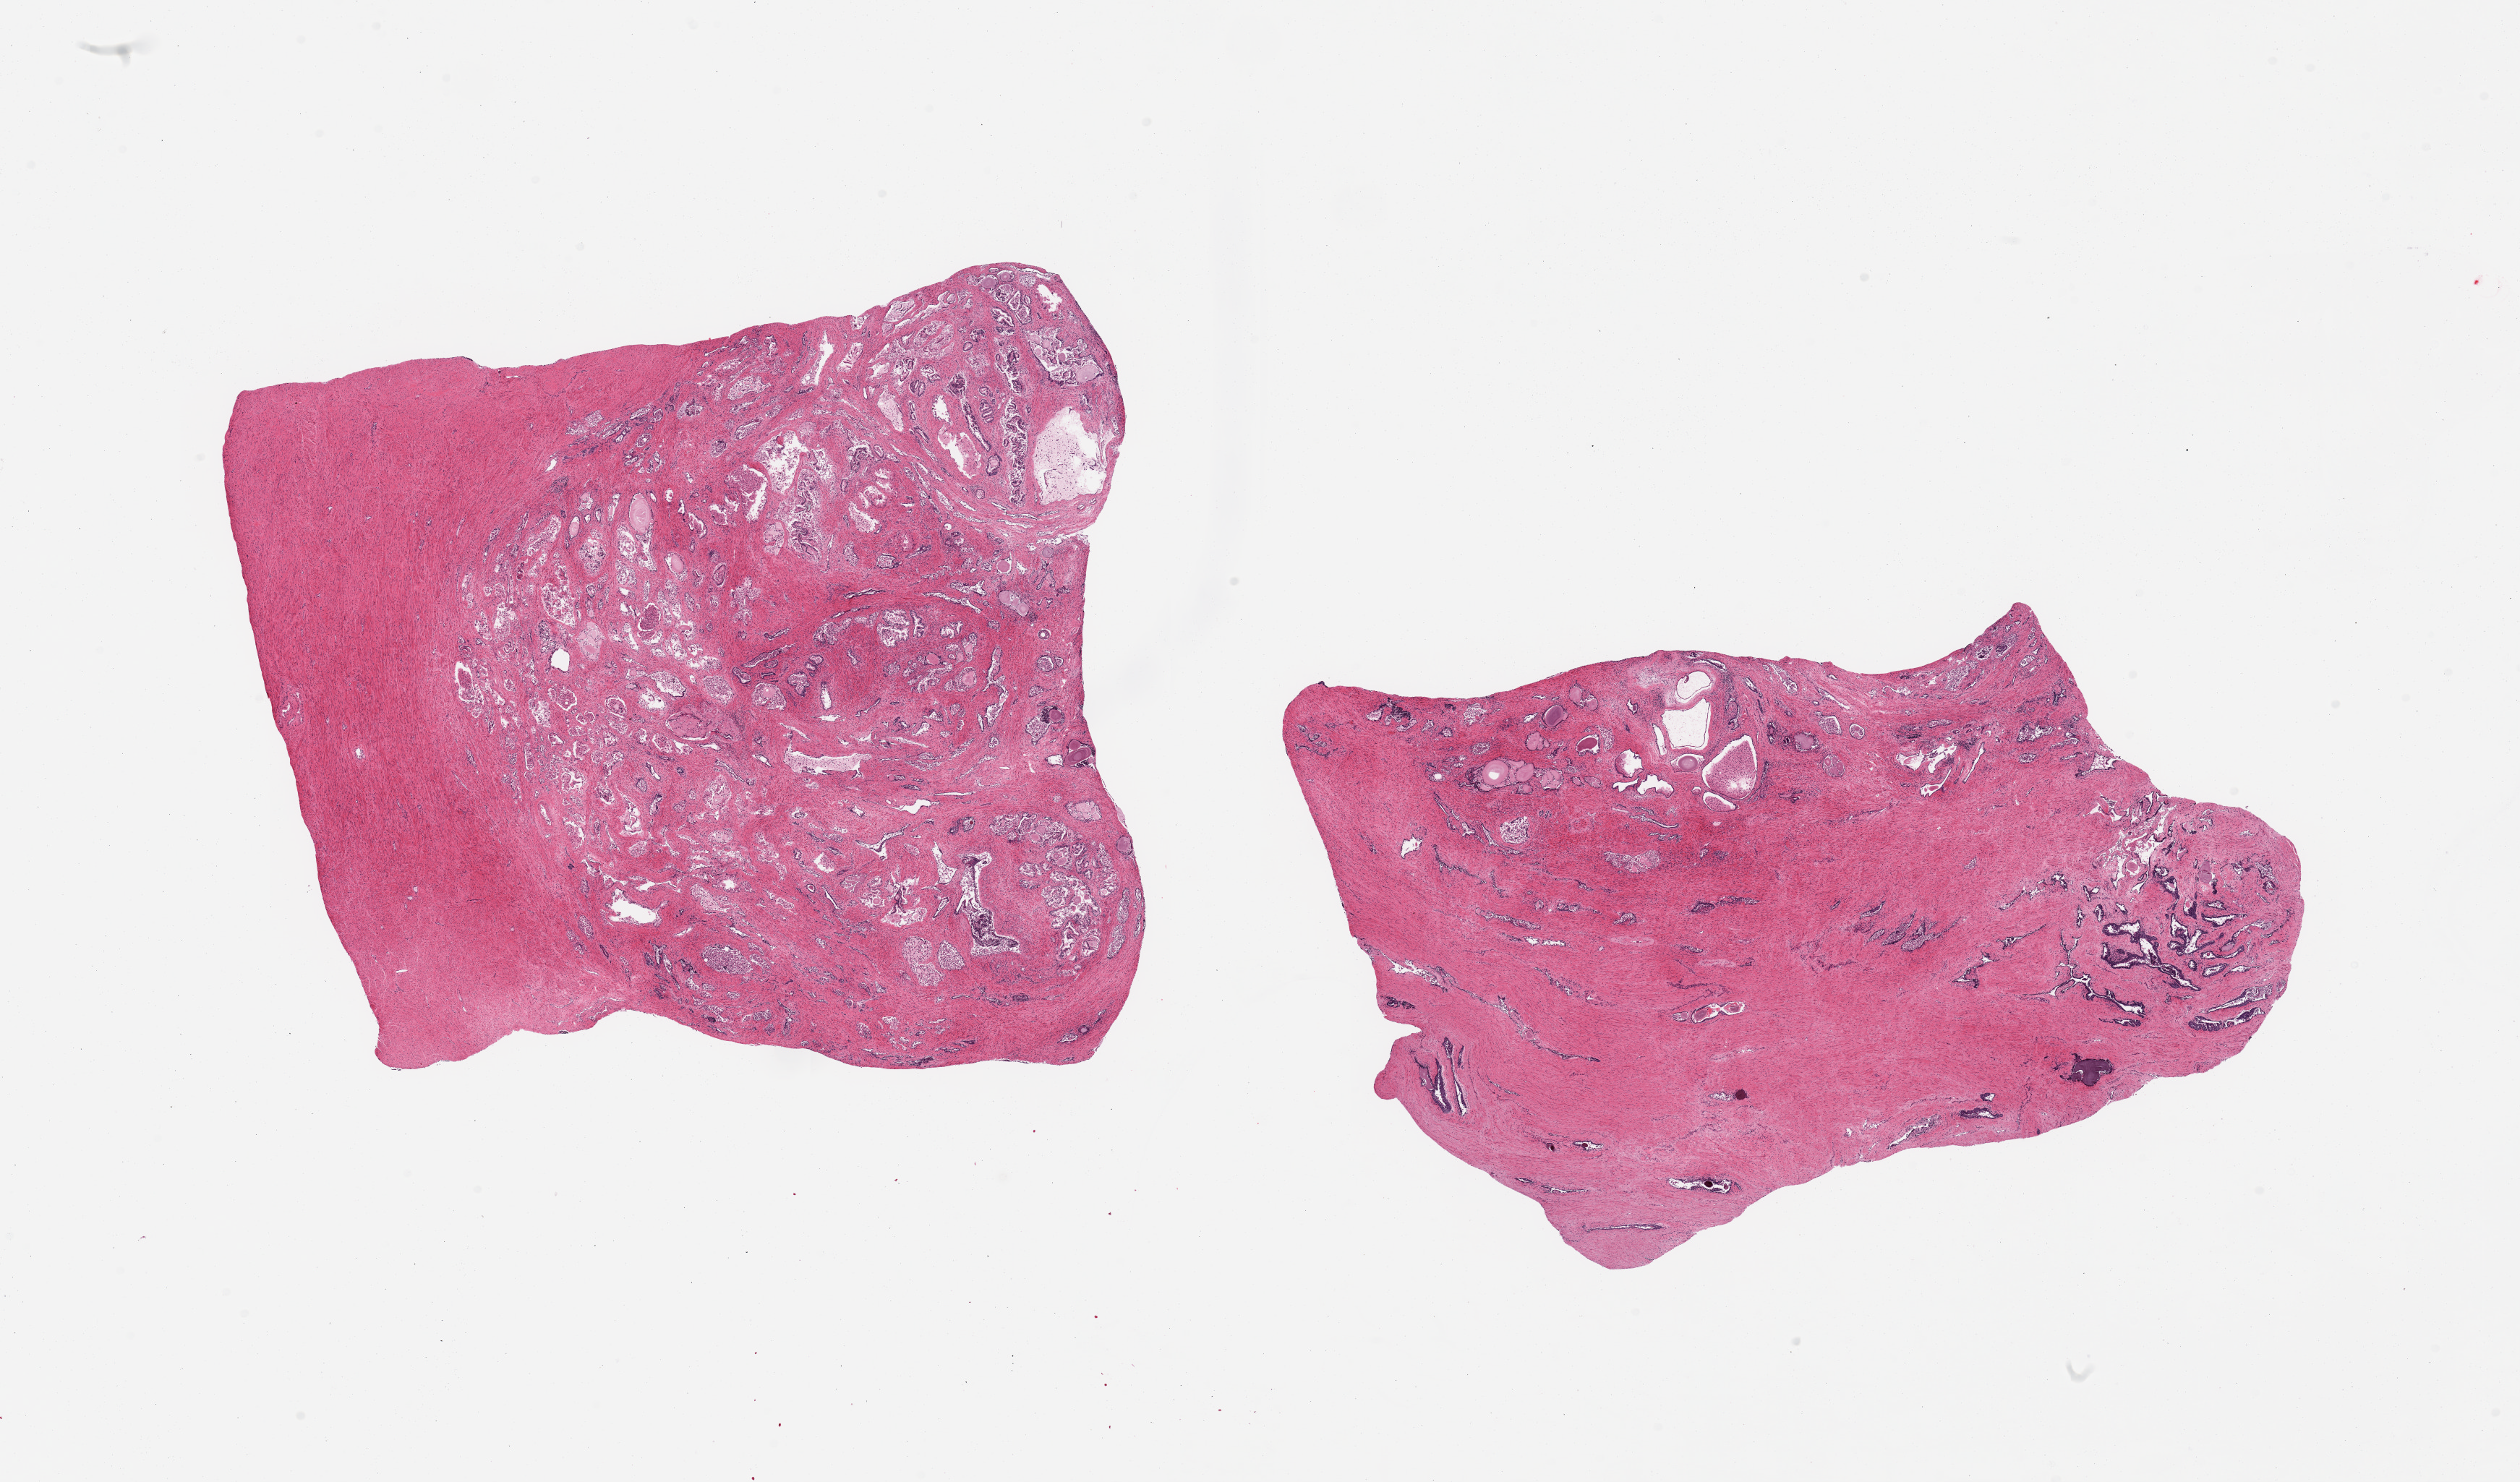
Digitized haematoxylin and eosin-stained section — low-resolution overview of the scanned area, about 27.6 x 16.2 mm (slide scanned at 20x); PAXgene-fixed, paraffin-embedded tissue; target tissue: prostate; donor tissue sample. Donor: male.
* reviewer comment on this tissue sample: 2 pieces; fibromuscular stroma and glandular component with sloughed epithelial cells; amylaceous bodies